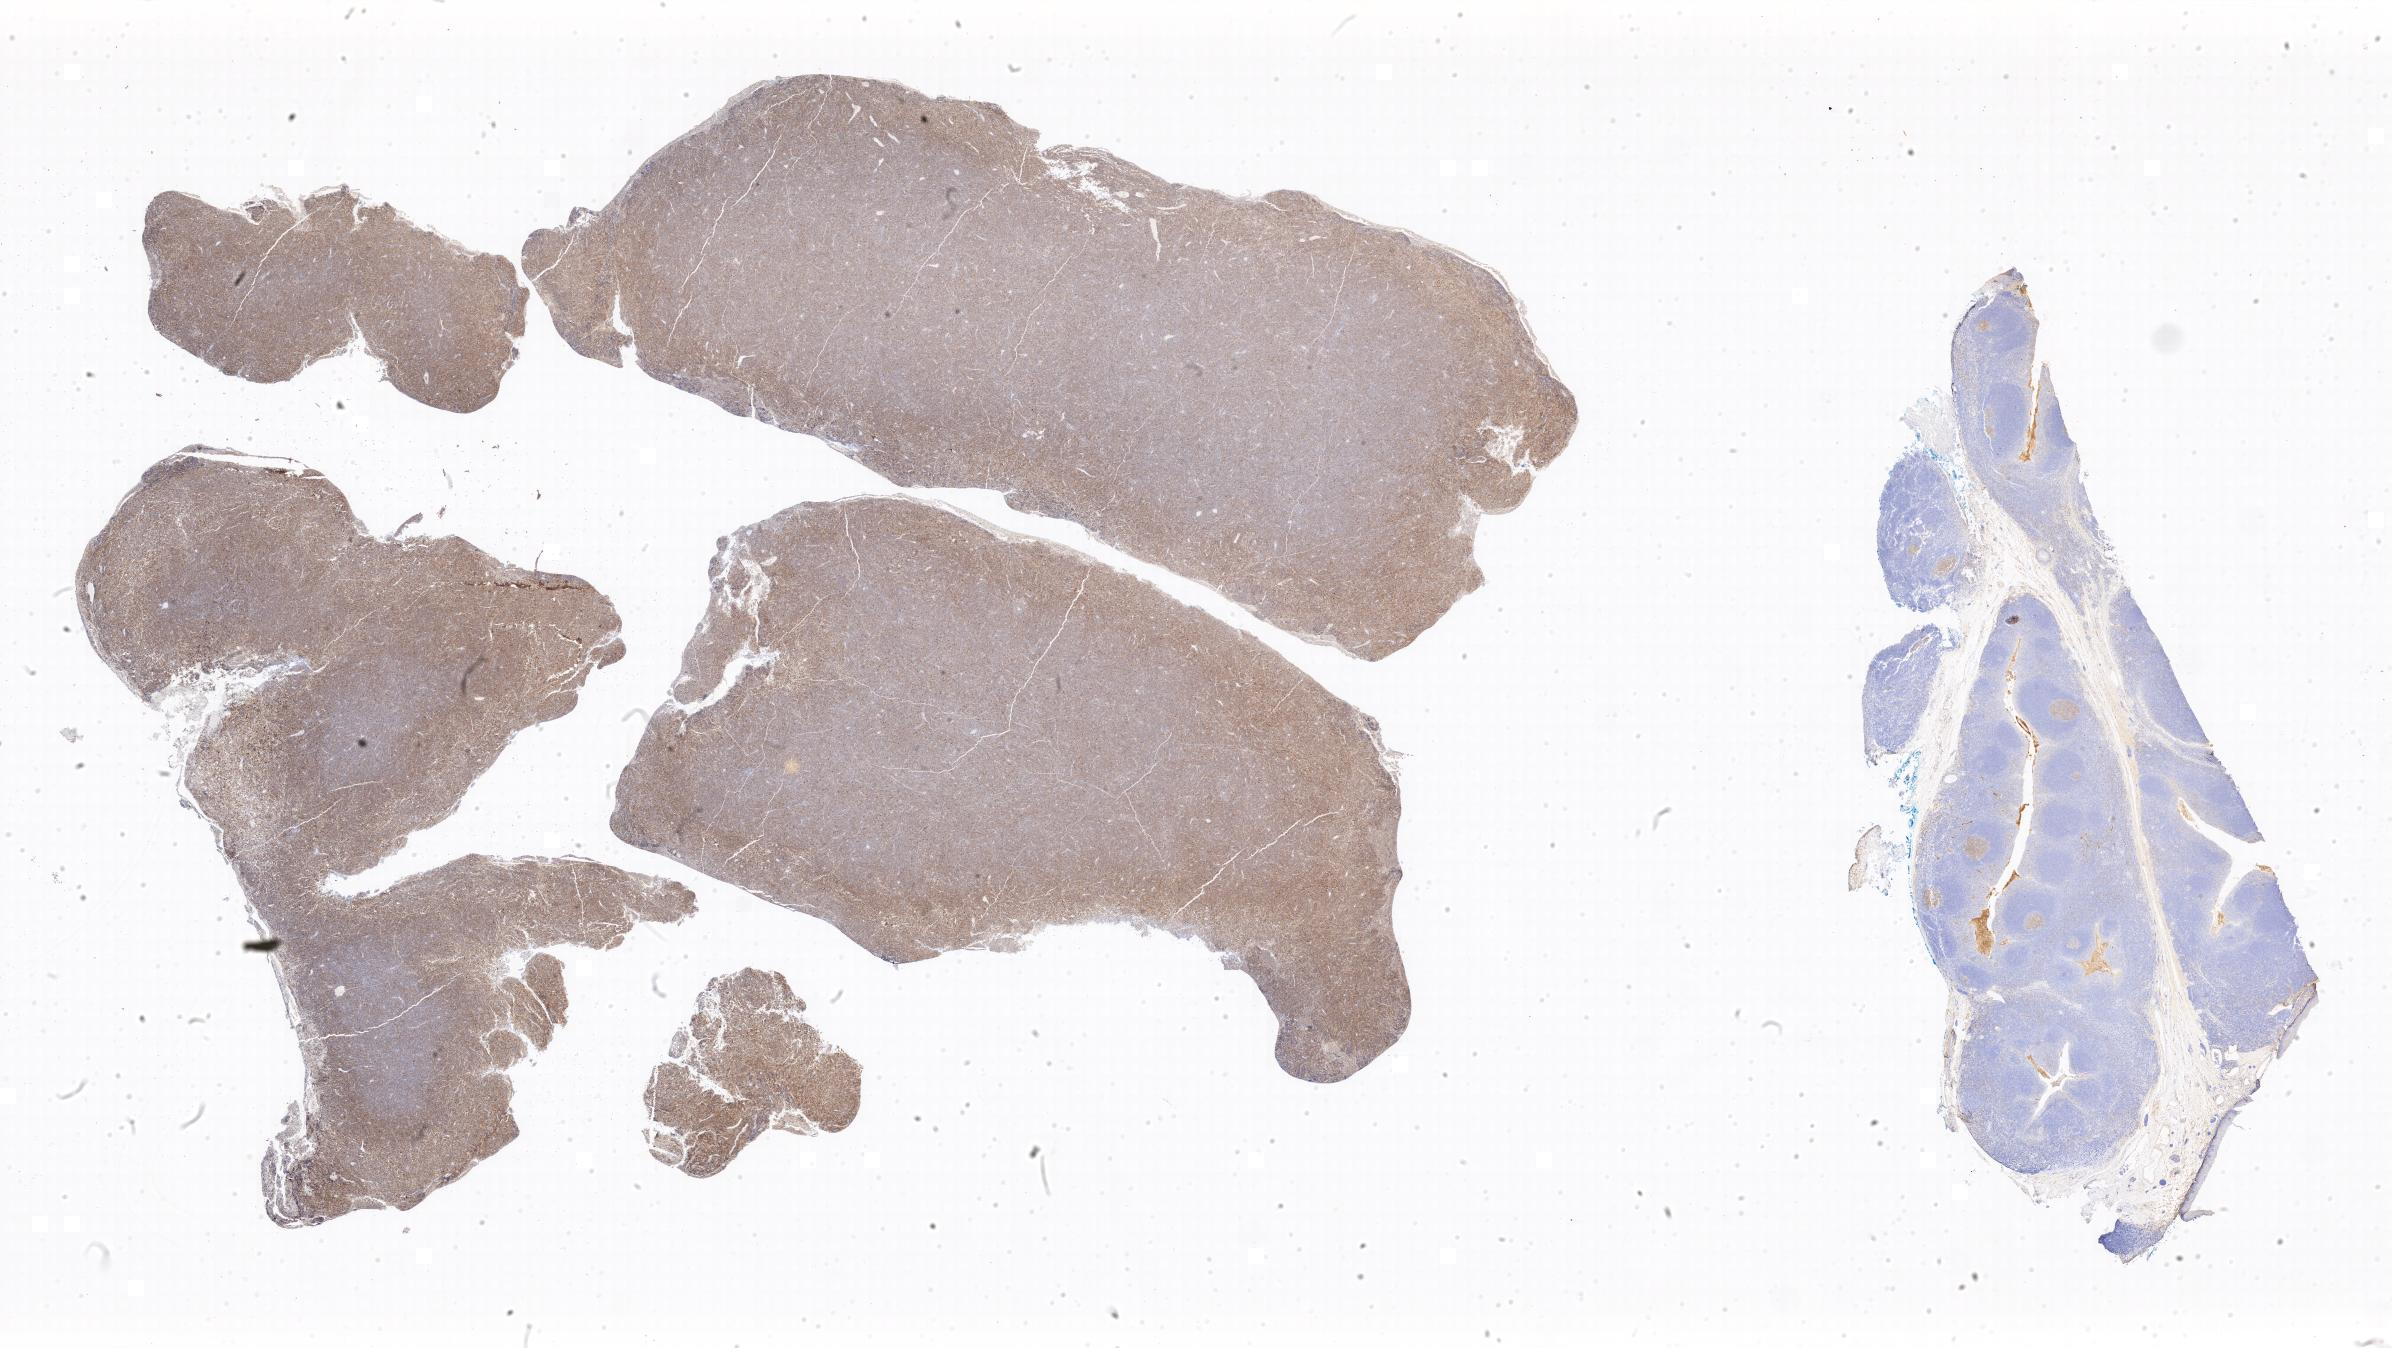
IHC for CD10, whole-slide image — whole scanned area shown as a low-resolution overview, specimen: tumor tissue, site: peritoneum. Female patient; age at initial diagnosis 7 years.
* histologic diagnosis: Burkitt lymphoma, NOS